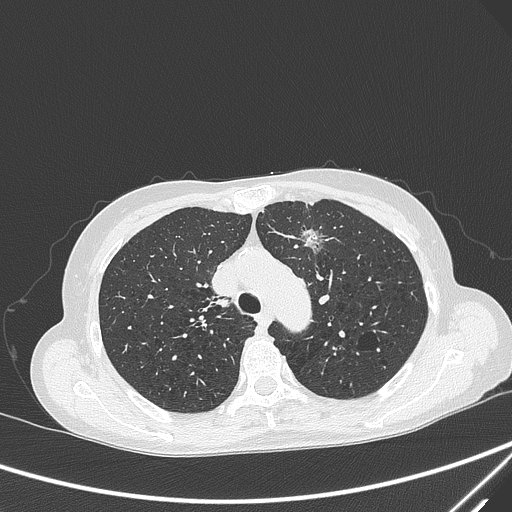
Chest CT, one axial slice. Slice 221 of 299 in the series (ordered by position). Lung window (W 1500 / L -600 HU). 1 mm slice thickness. 512 × 512 image matrix, field of view 350 × 350 mm. Patient: female, 71 years. Case-level facts recorded for this patient, not image findings: clinical TNM (as recorded): T1c N0 M0; histopathological grade: G2-3.
Structures marked on this image (bounding box drawn by a radiologist):
- lung tumour (recorded histology: adenocarcinoma): bounding box <296,223,331,255> (left, top, right, bottom; pixels)